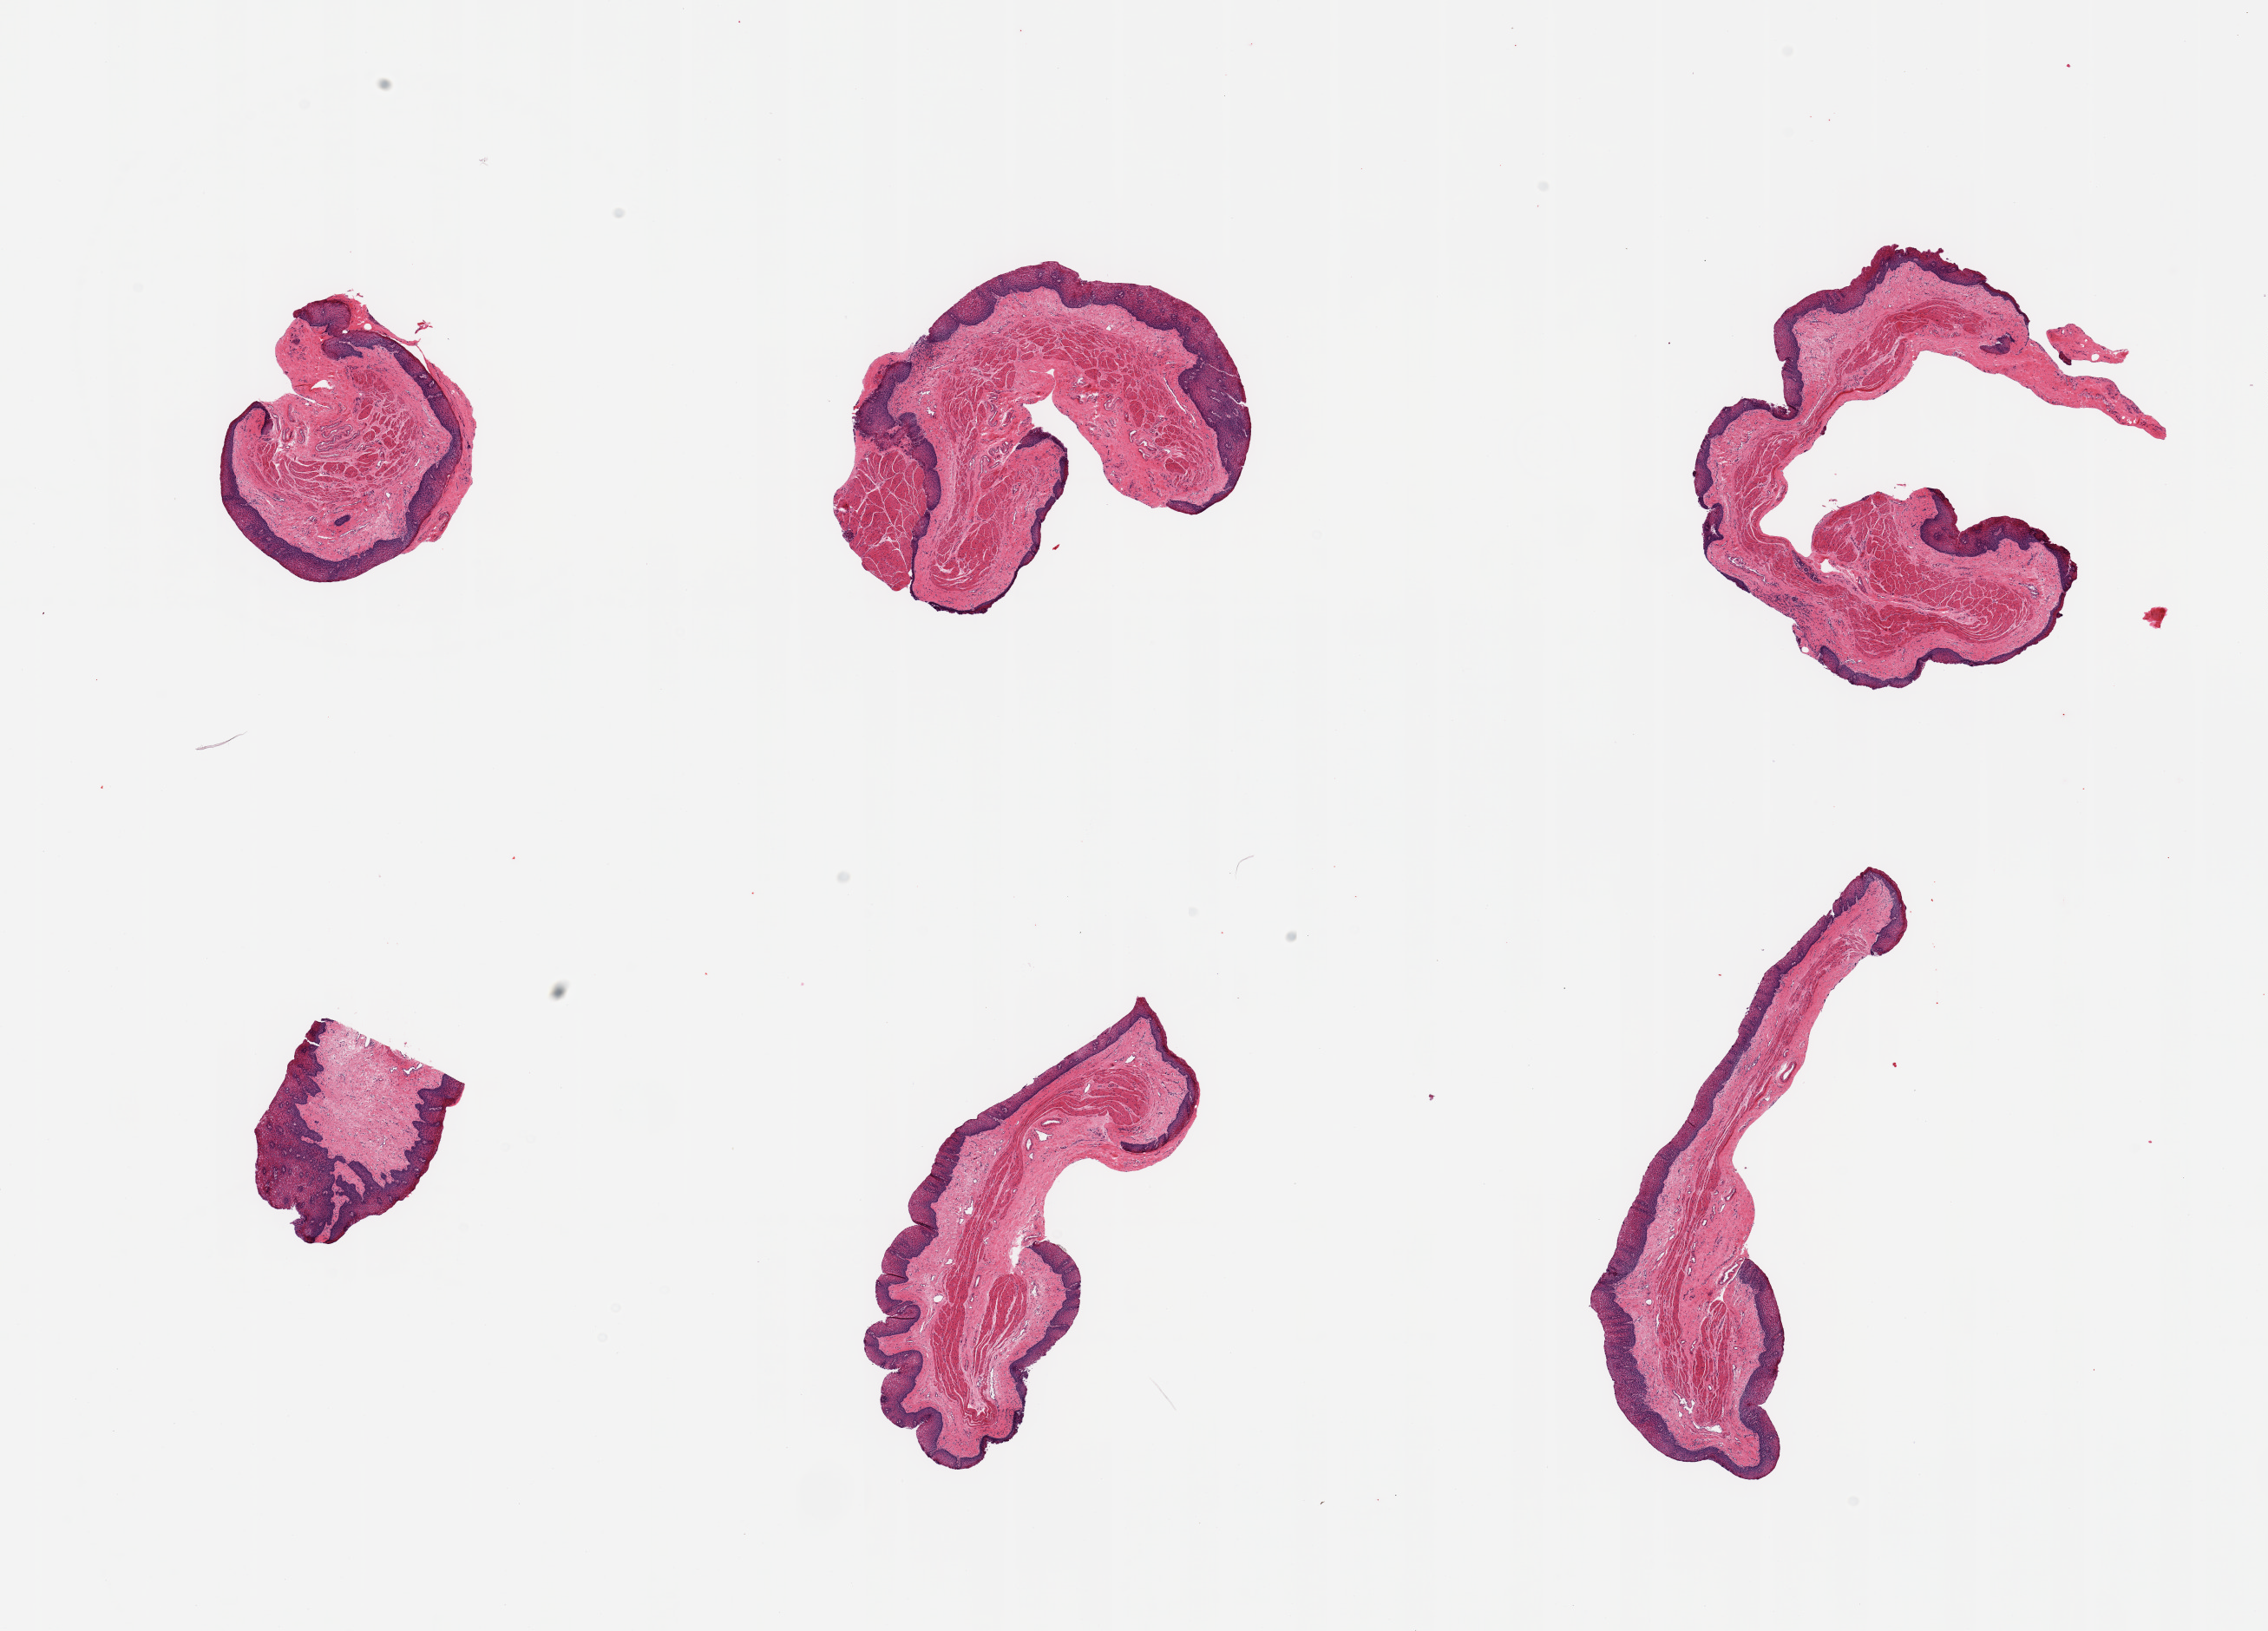
Whole-slide image, hematoxylin and eosin (H&E) stain, brightfield — low-resolution overview of the scanned area, about 20.7 x 14.9 mm (slide scanned at 20x); PAXgene-fixed paraffin-embedded (PFPE) section; section of esophageal mucous membrane (target tissue); tissue donor sample. Donor sex: female.
Reviewer comment on this tissue sample: 6 pieces; prominent muscularis mucosae in 5 of 6 pieces; well dissected.